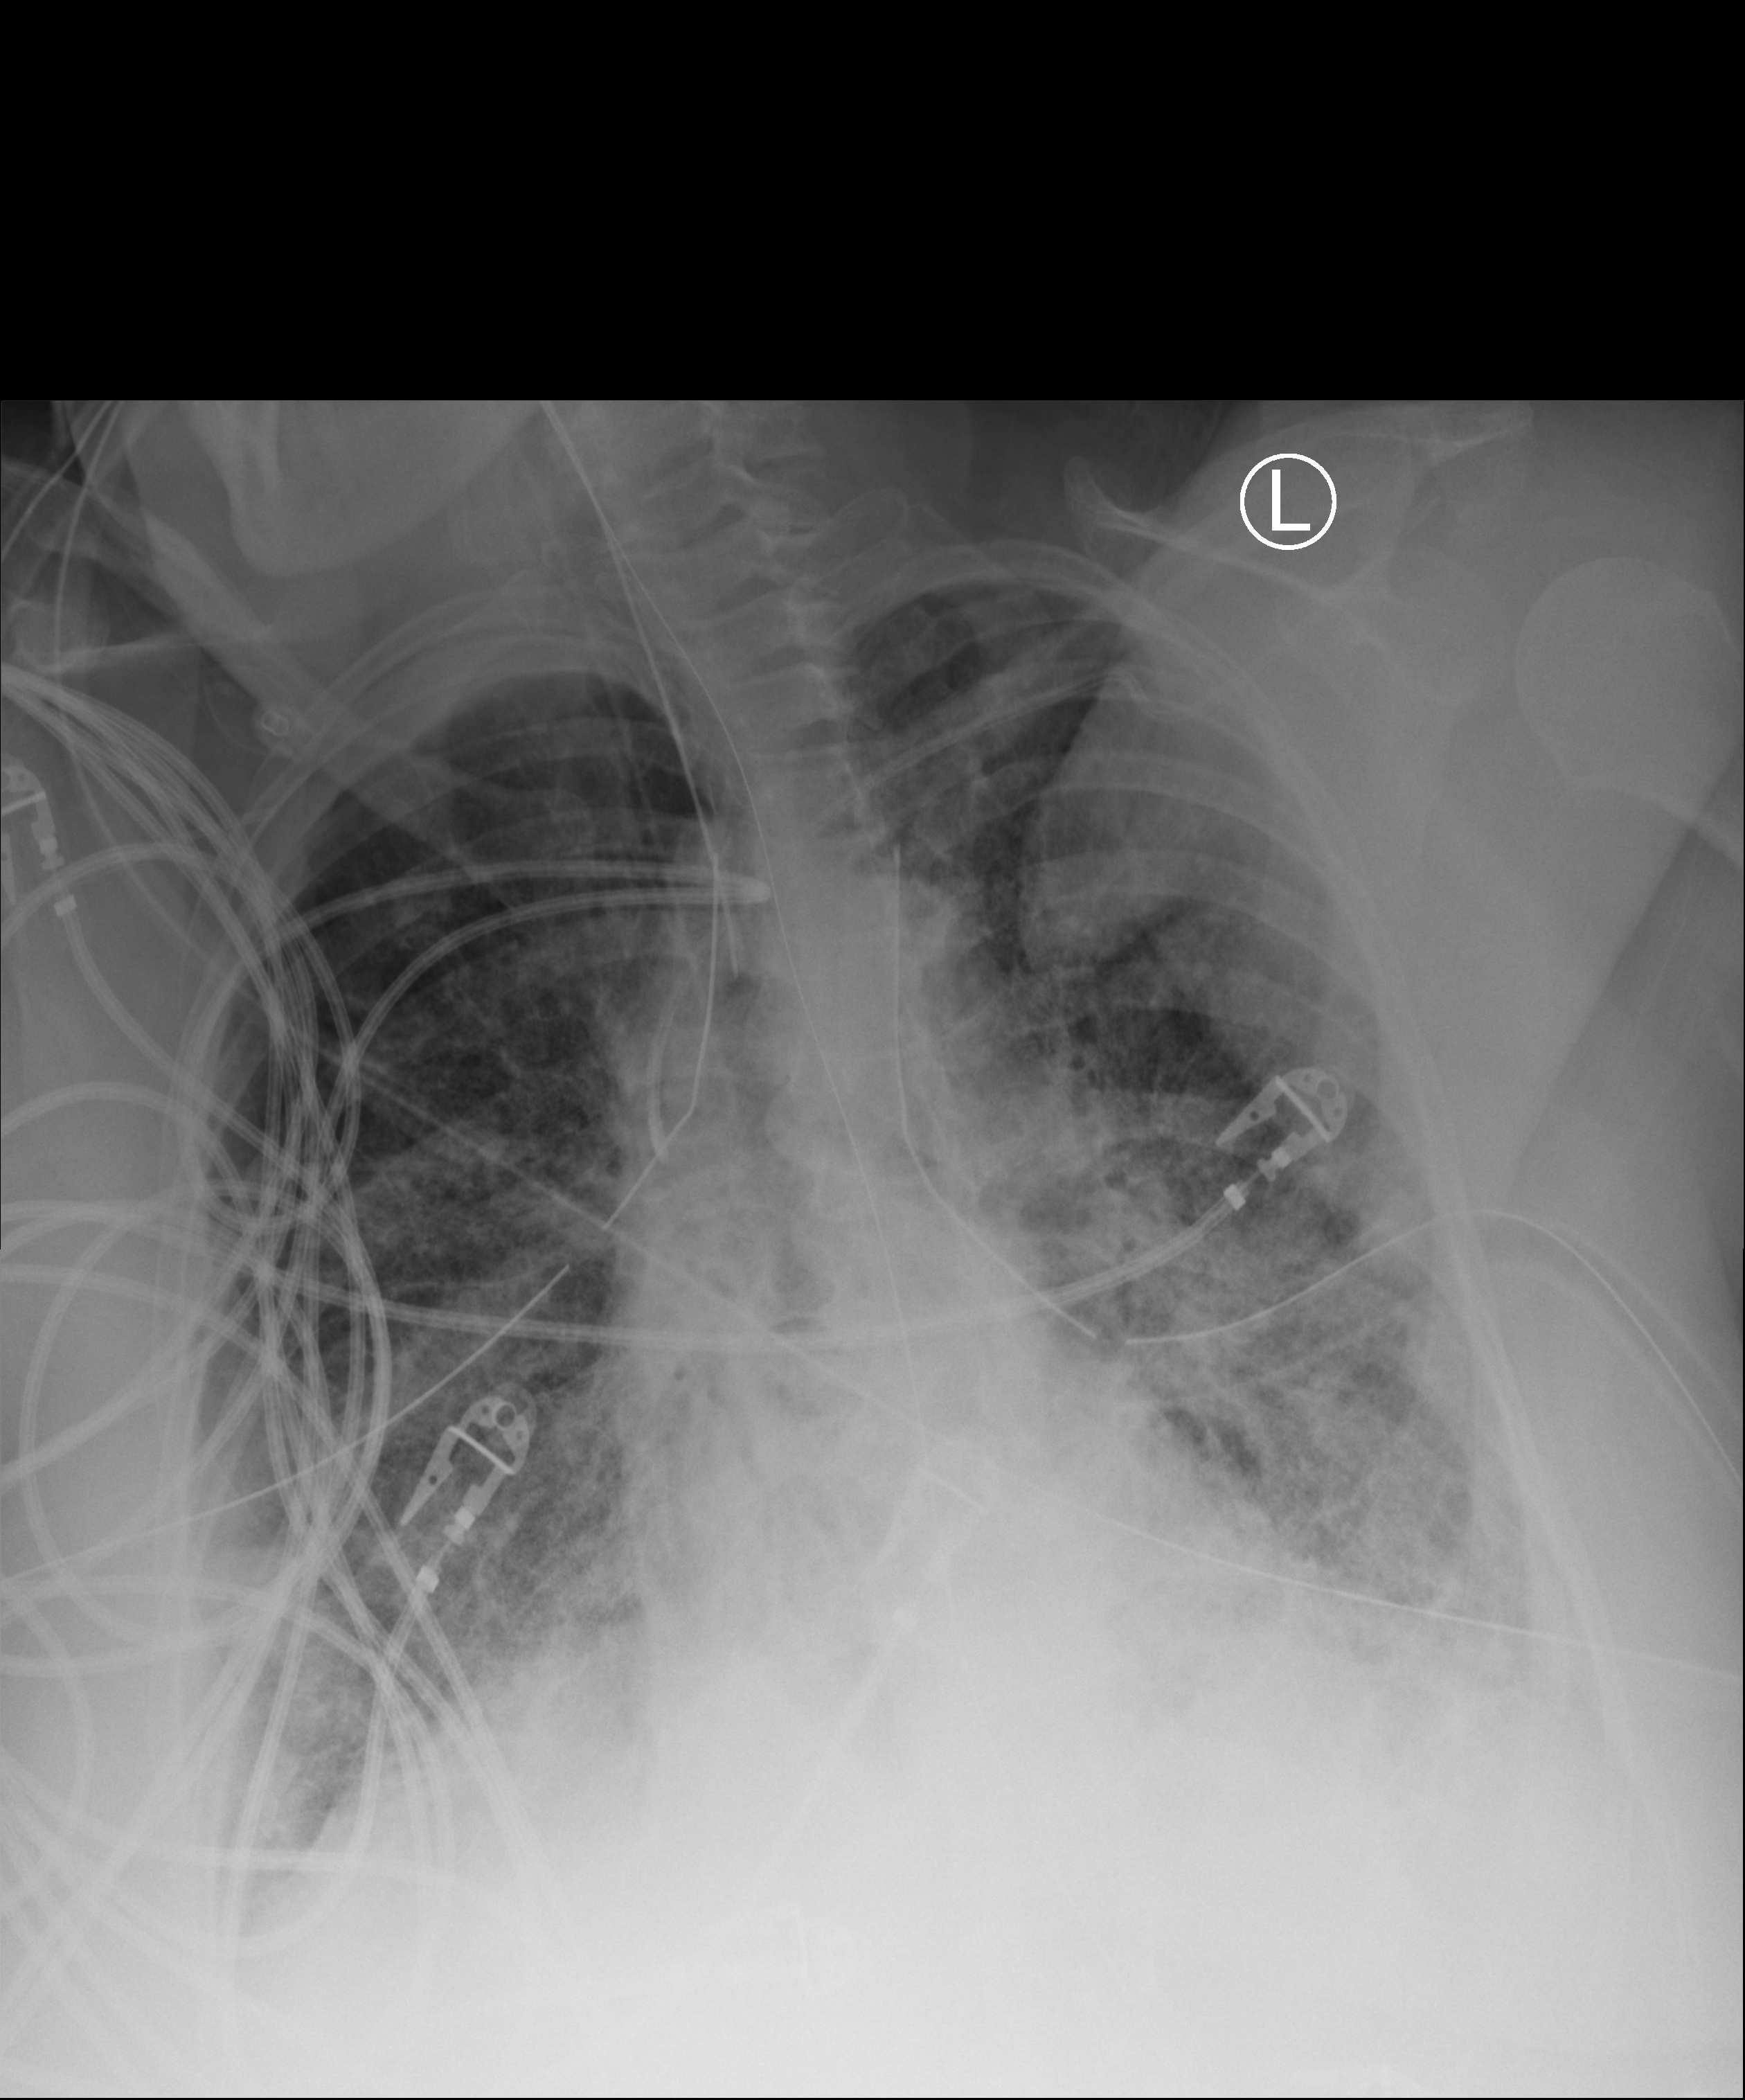
Chest X-ray (portable); anteroposterior (AP) projection. Patient hospitalised with COVID-19; female, aged 60–74 years.
From the hospital-stay record, not from the radiograph (when in the stay this image was taken is not recorded): smoking status (admission record): former; mechanically ventilated during this hospital stay: yes.